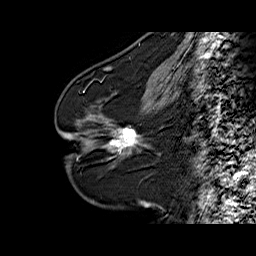
Breast MRI (dynamic contrast-enhanced), one sagittal slice; slice 28 of 60 in the series (ordered by position); dynamic contrast-enhanced series, time point 2 of 6 at this slice position (early post-contrast); 1.5 T; TE 6.3 ms, TR 32.5 ms; 4 mm slice thickness; 256 × 256 image matrix, field of view 200 × 200 mm. Female patient. From the clinical record (not read from this slice): setting: breast cancer imaged before/during neoadjuvant chemotherapy; receptor status: HR-positive, HER2-negative.
Outlined on this slice (semi-automatic segmentation, software-assisted and operator-edited):
- analysis volume of interest (the breast-tissue region the enhancement analysis was run in; not a lesion): bounding box [x1, y1, x2, y2] px = [94, 103, 161, 160]
- tumour enhancement mask (voxels above the 100 % enhancement threshold inside the analysis volume of interest): [110, 129, 138, 151]